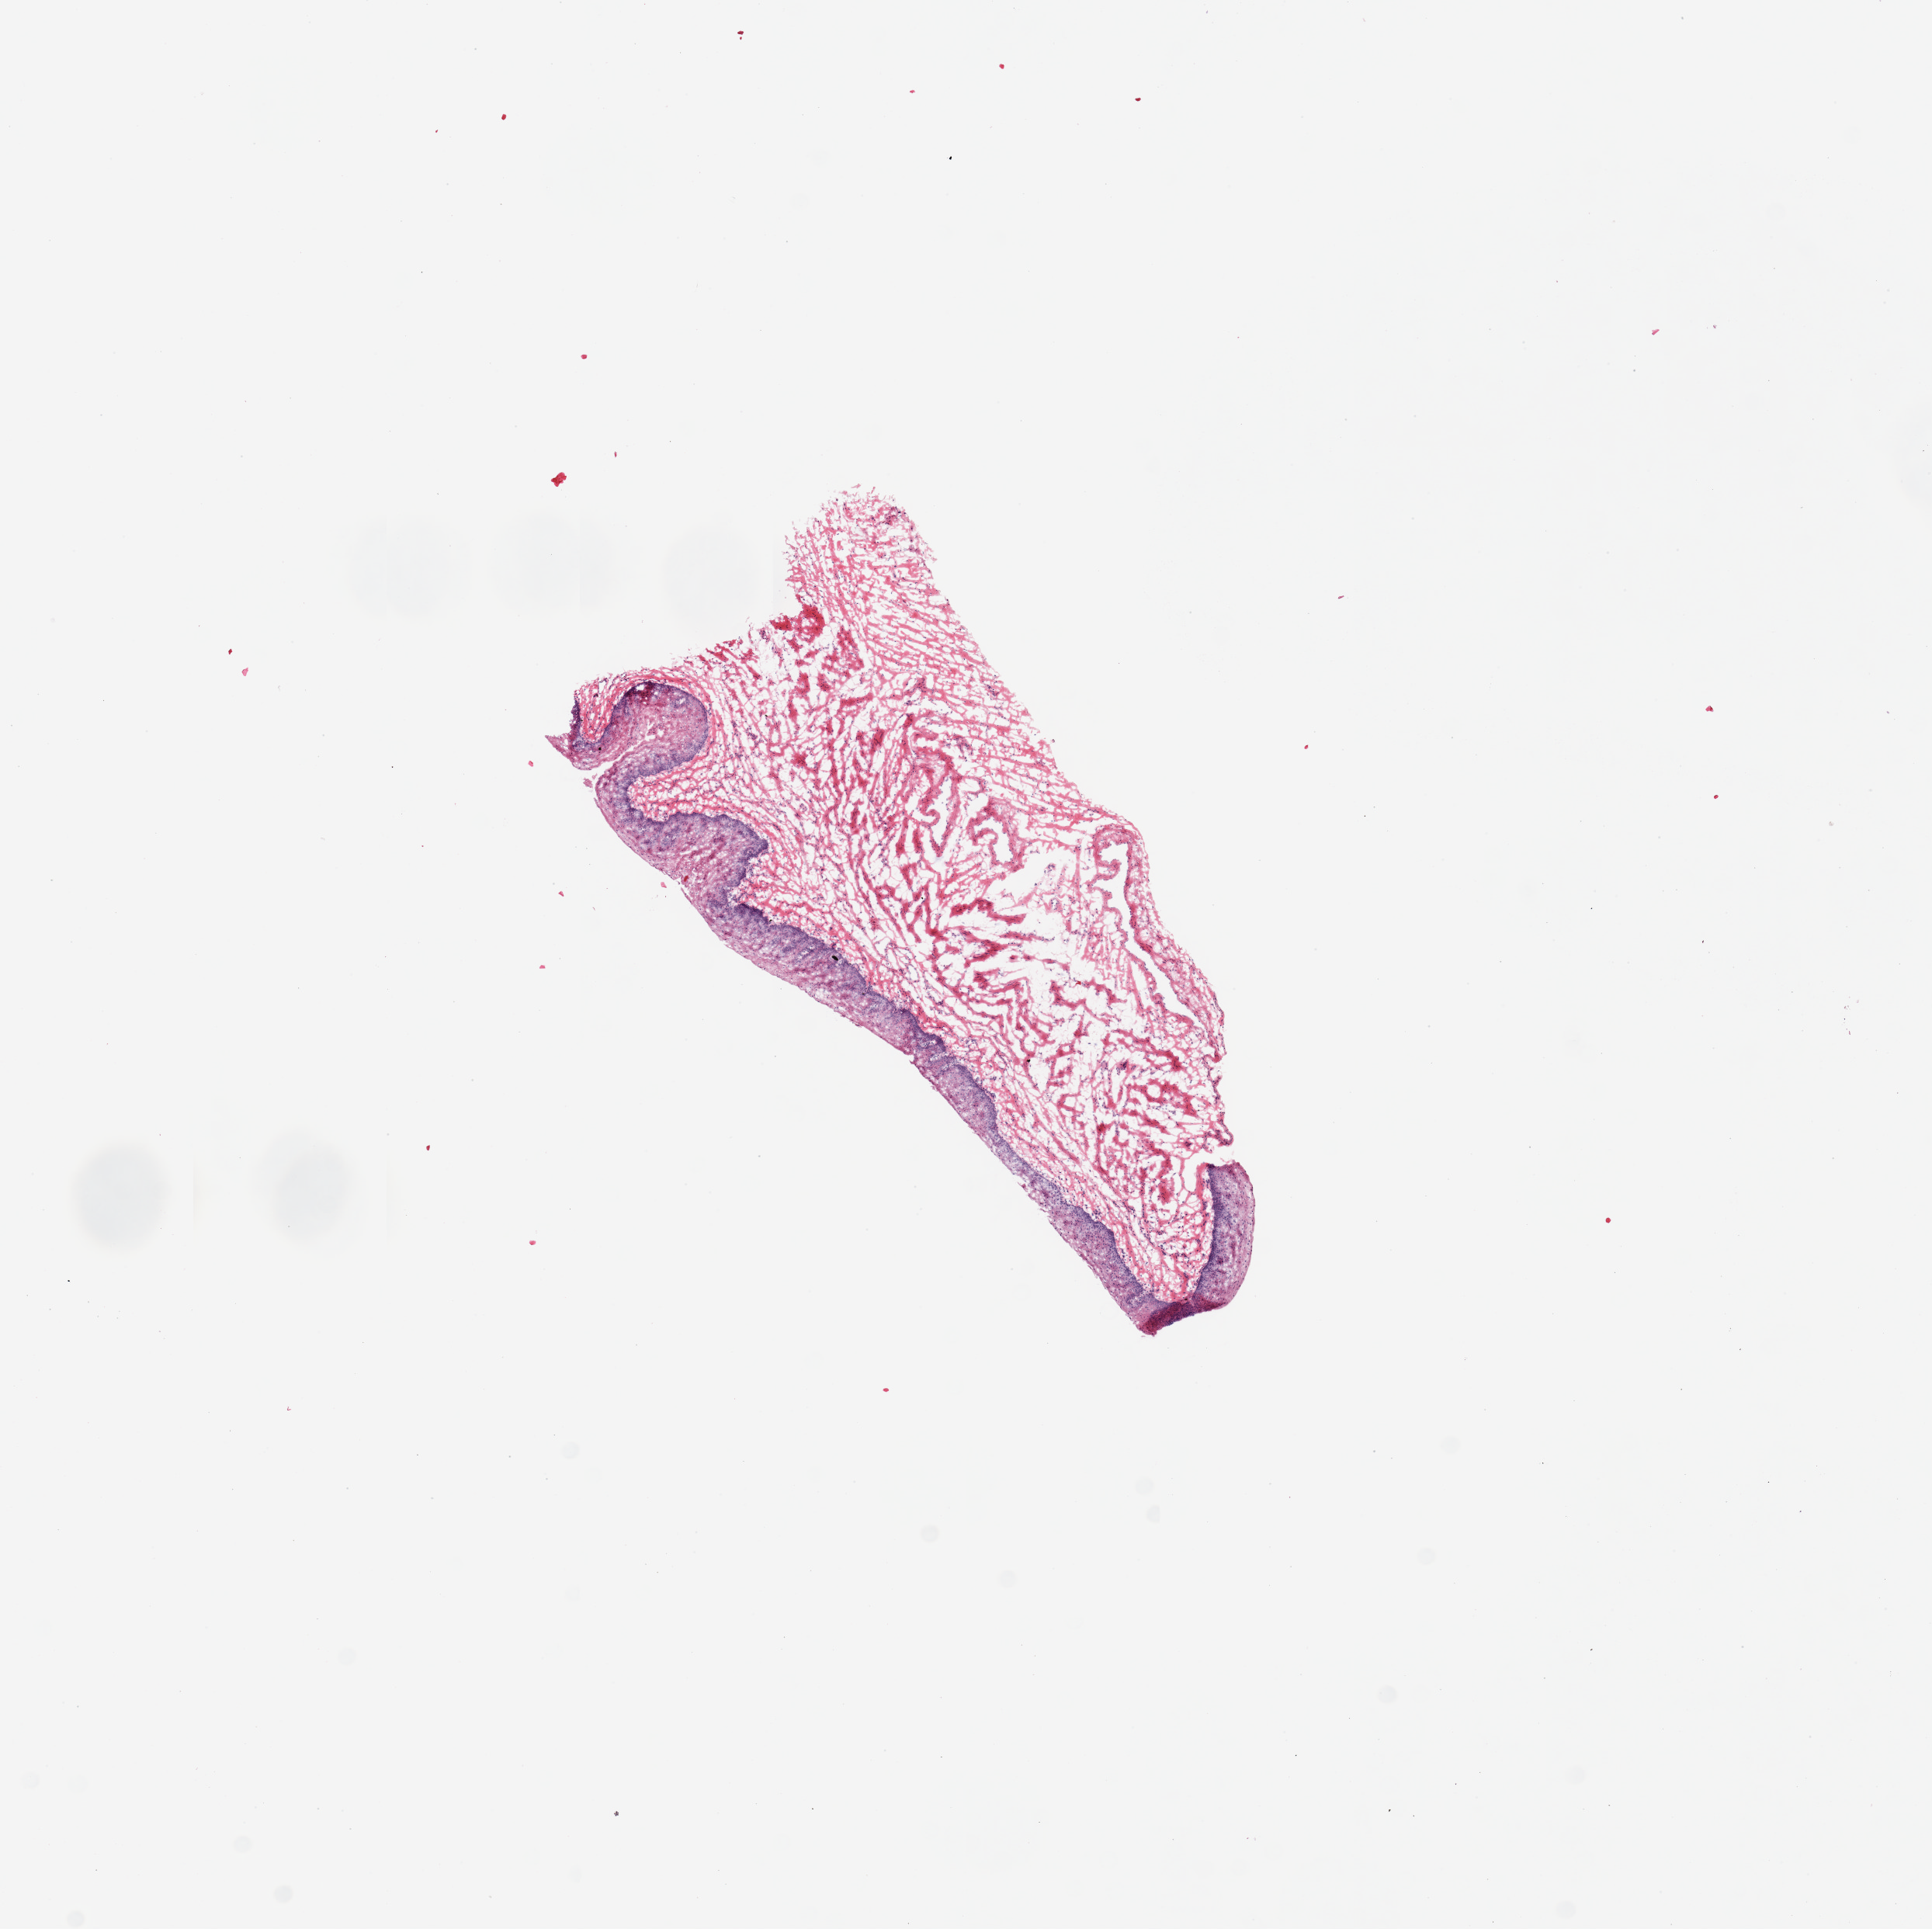
Digitized H&E-stained section — low-resolution overview of the scanned area, about 9.8 x 9.8 mm (acquisition: 20x scan).
Specimen: frozen section; sampled site (target tissue): esophageal mucous membrane; donor tissue sample.